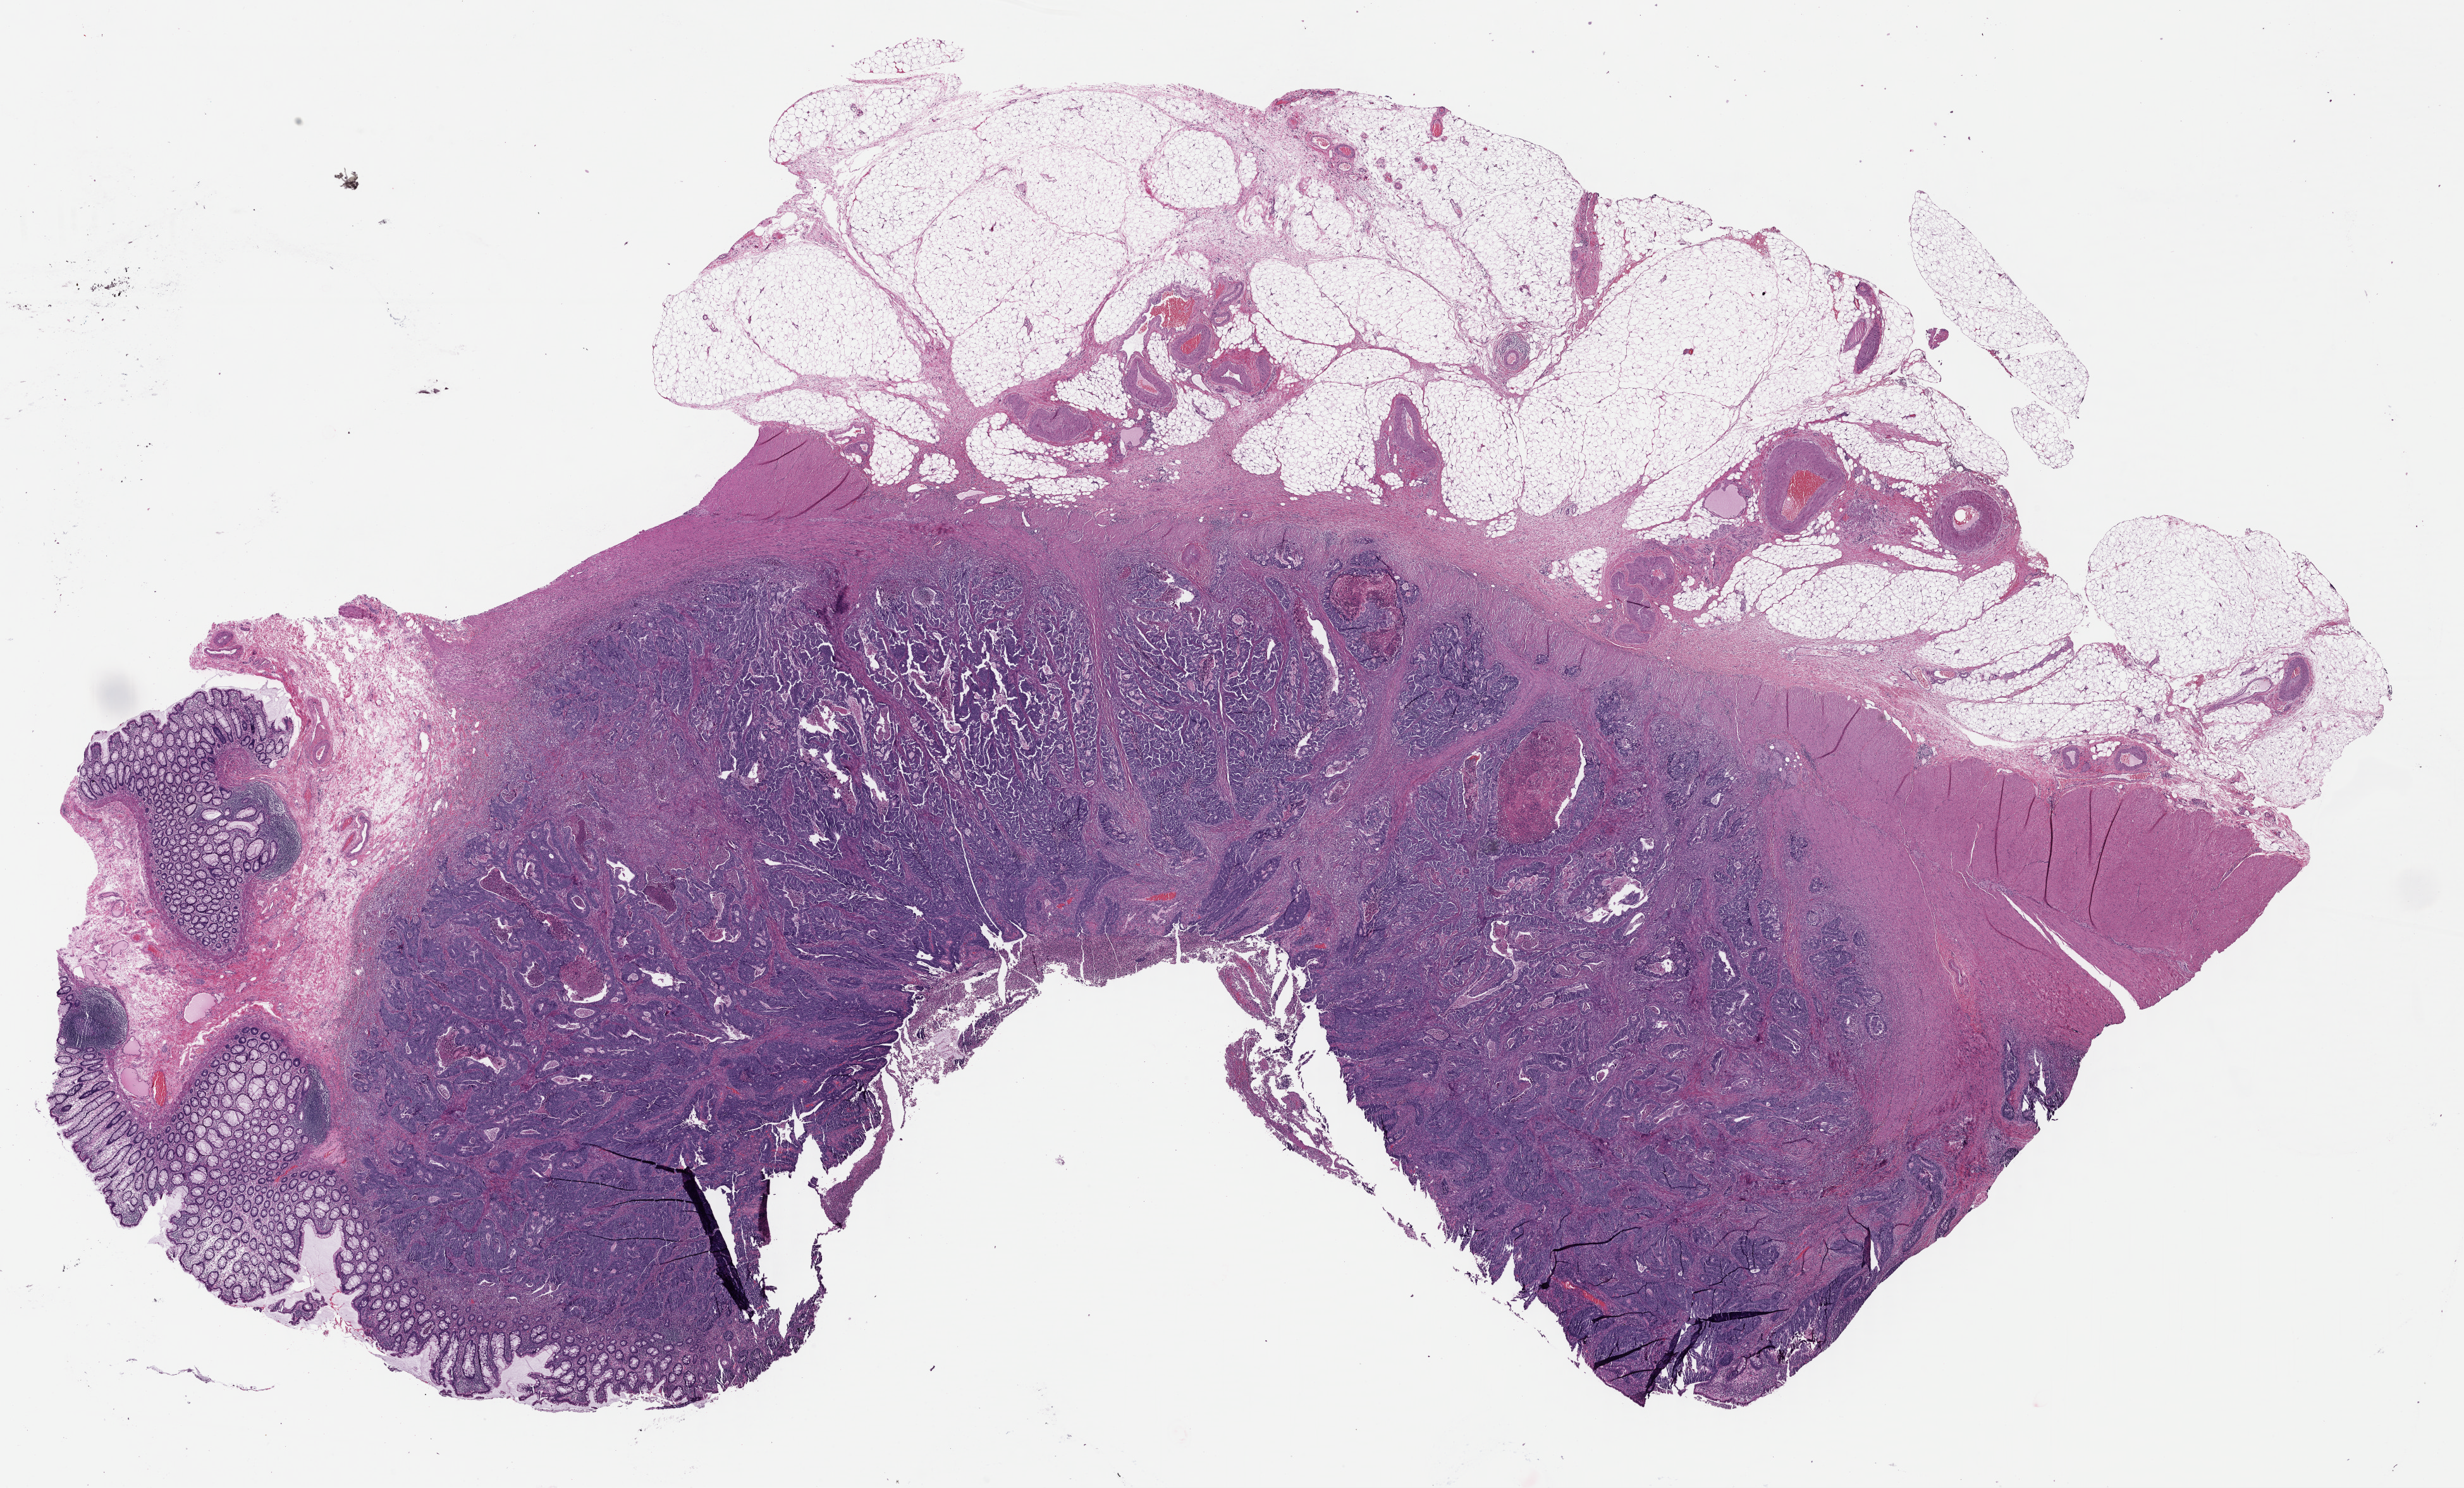
H&E-stained whole-slide image — a low-resolution overview of the entire scanned area, about 30.6 x 18.5 mm. FFPE section. Sample: primary tumour, colon. Female, age 68 years at initial diagnosis.
Diagnosis: Adenocarcinoma, NOS. AJCC pathologic stage: IIA (7th edition).